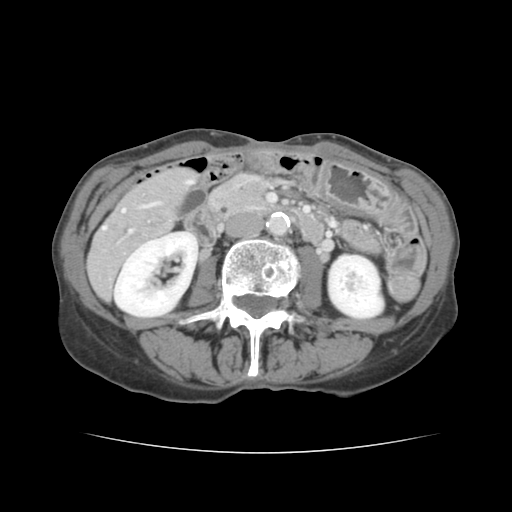
Contrast-enhanced abdominal CT, one axial slice; slice 43 of 136 in the series (ordered by position); 120 kVp; intravenous contrast given; soft-tissue window (W 400 / L 40 HU); 2.5 mm slice thickness; 512 × 512 image matrix. Female patient, age 77 years. Case-level facts recorded for this patient, not image findings: diagnosis: colorectal cancer liver metastases, imaged before liver resection; multiple liver metastases: yes; largest metastasis: 3 cm; disease in both lobes: no.
Annotated regions visible in this slice (manually delineated by an expert):
- hepatic veins: box from (x=103, y=181) to (x=193, y=230) px
- liver: (x=89, y=168)–(x=195, y=297)
- planned liver remnant (the part of the liver to remain after resection): (x=177, y=169)–(x=193, y=183)
- portal vein (with intrahepatic branches): (x=129, y=230)–(x=133, y=233)